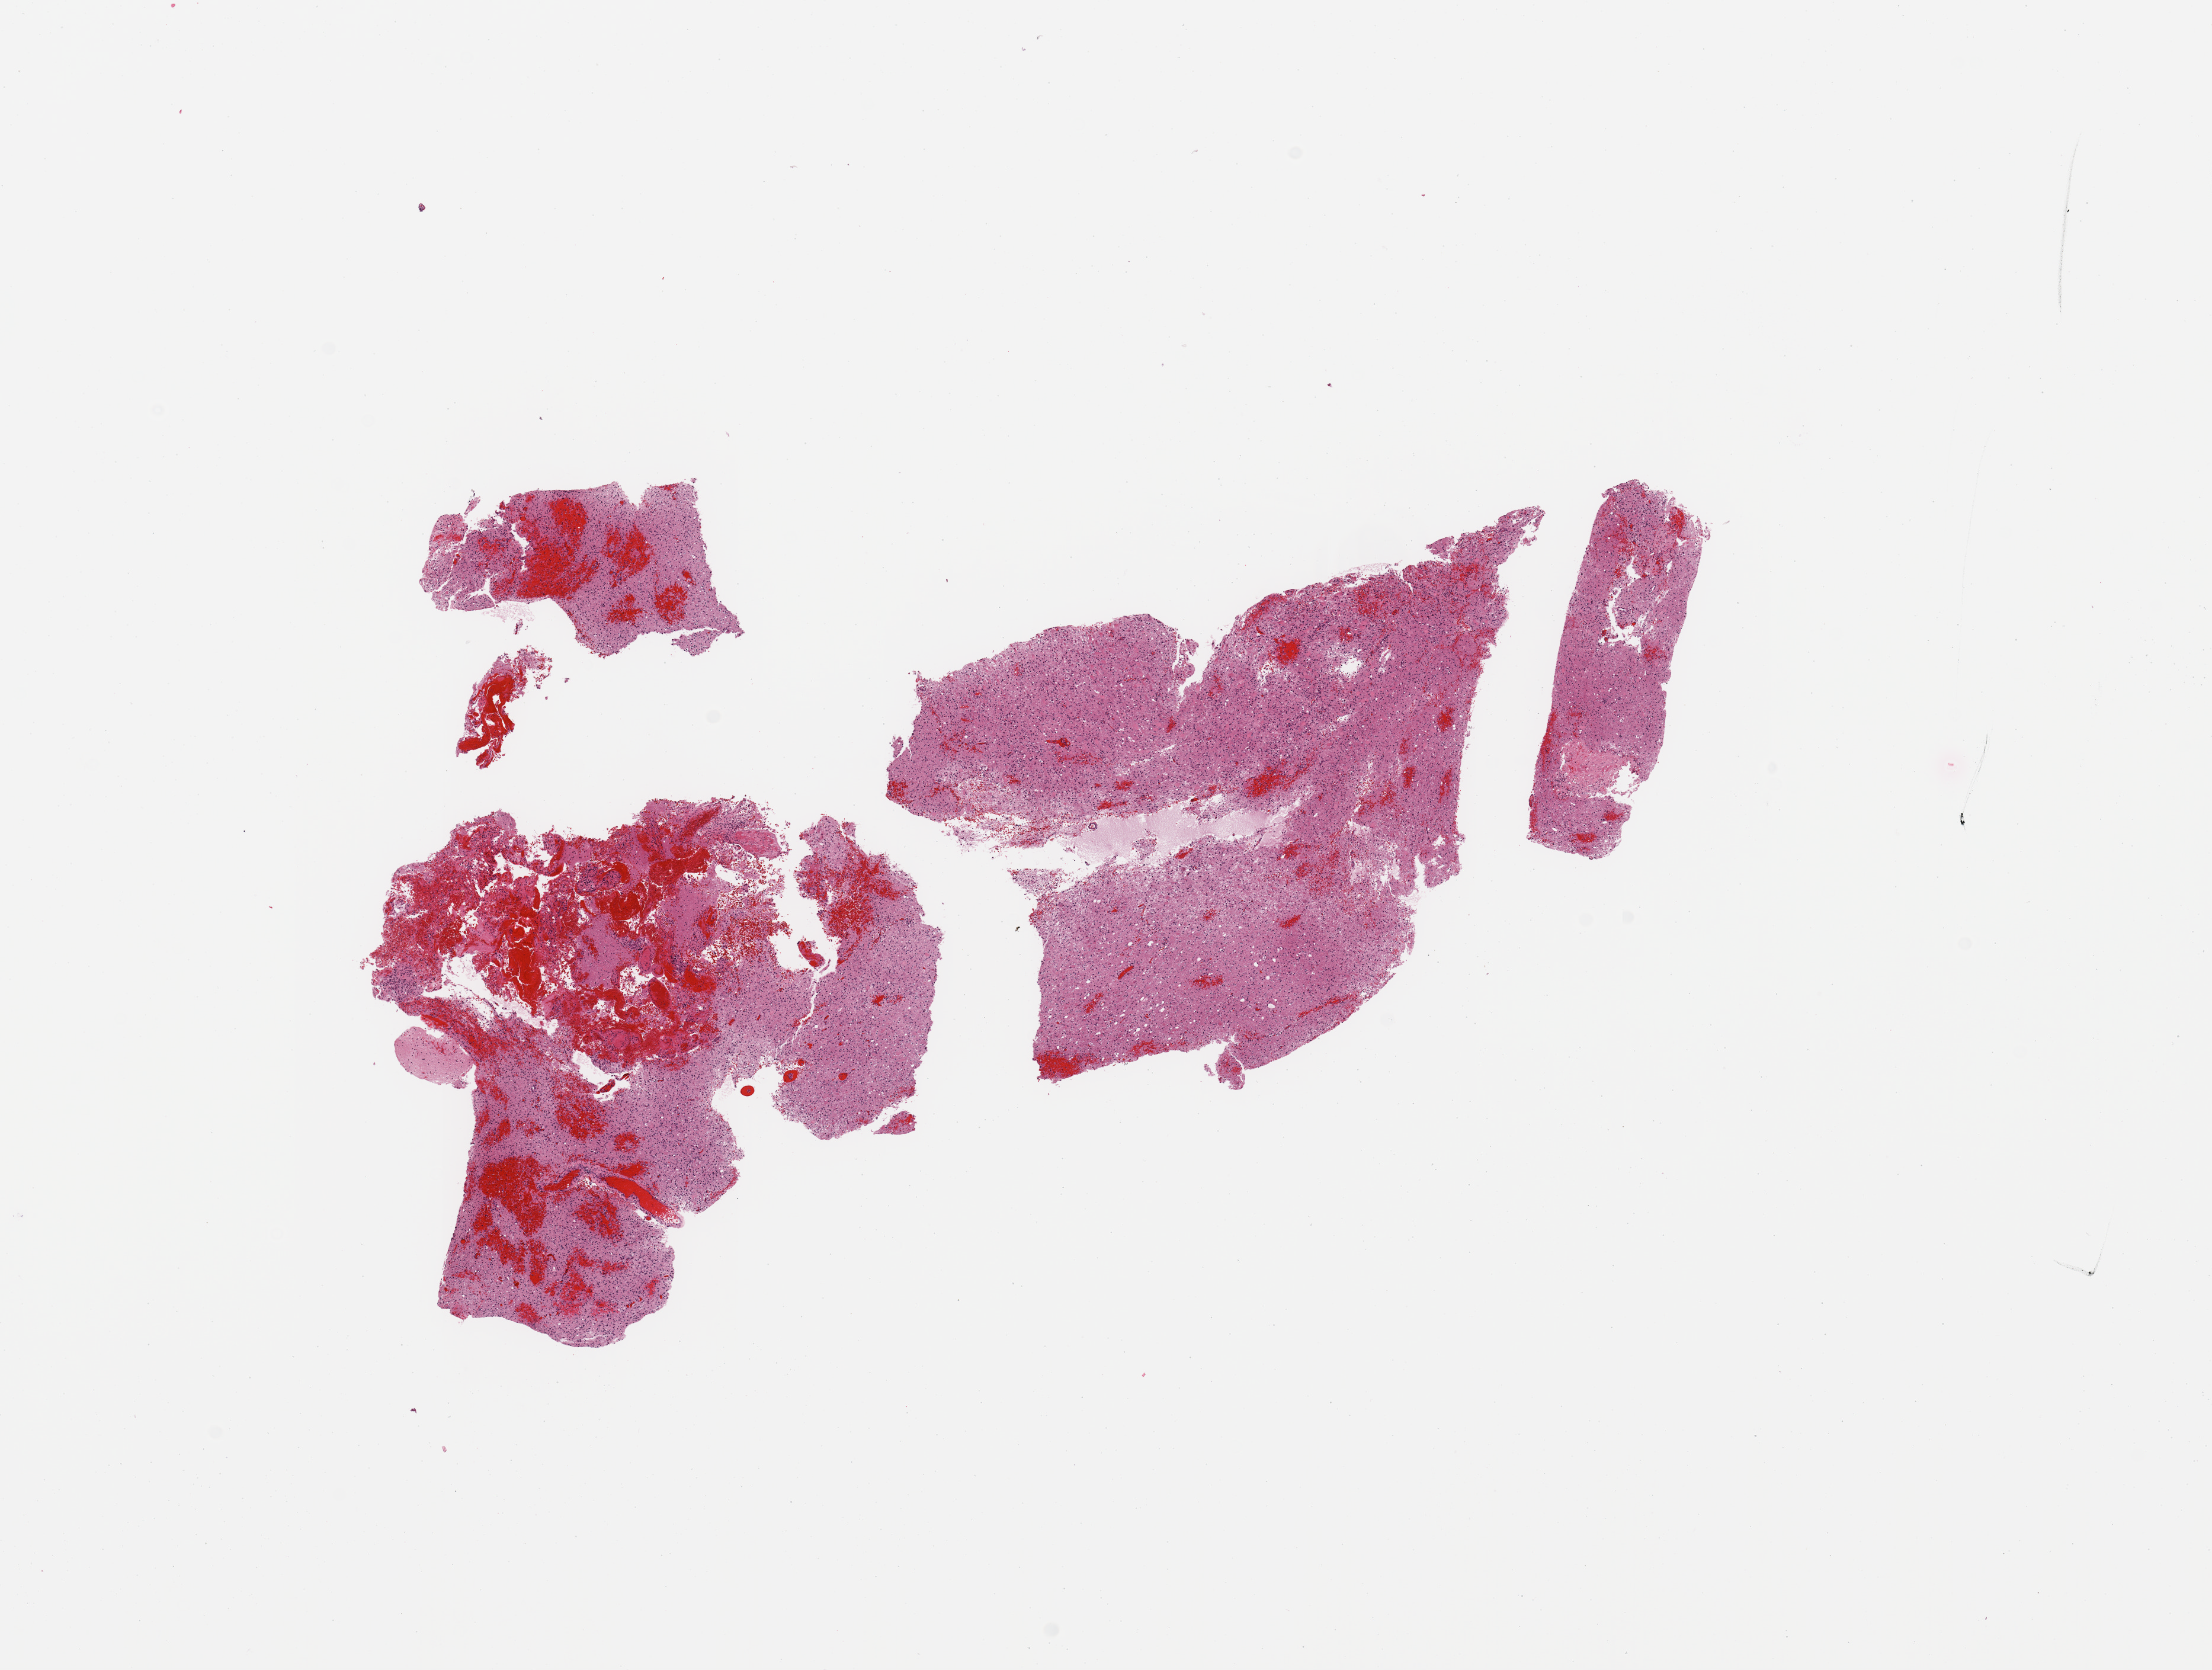
Digitized H&E tissue section (whole slide) — low-resolution overview of the scanned area, about 14.8 x 11.1 mm (slide scanned at 20x). Tumour tissue sample, sampled site: frontal lobe. 68-year-old female patient. Pathologist review of this section (percent, as recorded): tumour nuclei 80%, necrosis 15%.
* diagnosis: Glioblastoma